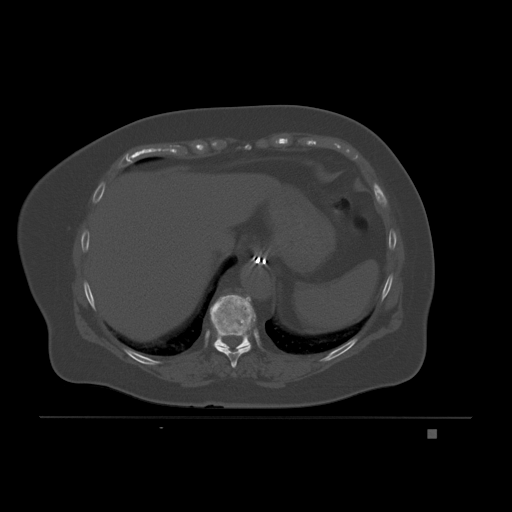
CT including the spine, one axial slice. Position 105 of 221 along the scan axis. Bone window (W 1800 / L 400 HU). 3 mm slice thickness. 512 × 512 image matrix, field of view 474 × 474 mm. Patient: female, 63 years. From the clinical record (not read from this slice): primary cancer: breast.
Structures marked on this image (semi-automatic segmentation, software-assisted and operator-edited):
- T10 vertebra: bounding box (x1, y1, x2, y2) in pixels: (210, 295, 256, 350)
- T9 vertebra: (214, 344, 252, 368)